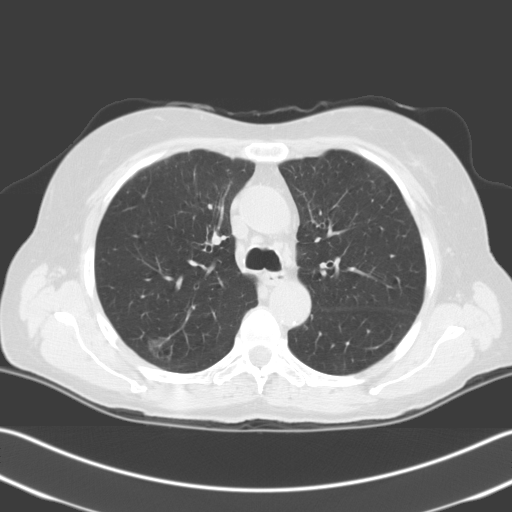
Low-dose screening chest CT, axial slice. Baseline annual screen. Lung window (W 1500 / L -600 HU). Standard (soft-tissue) reconstruction kernel (C). 140 kVp. 512 × 512 image matrix, field of view 348 × 348 mm. Female participant, aged 67 years at enrolment. Current smoker at enrolment.
- Expert reader's lesion annotation, bounding box <123,326,181,374> (left, top, right, bottom; pixels).
- The screening reader recorded 2 non-calcified nodules or masses ≥4 mm on this exam (right upper lobe, right upper lobe); which of them this box marks is not recorded.